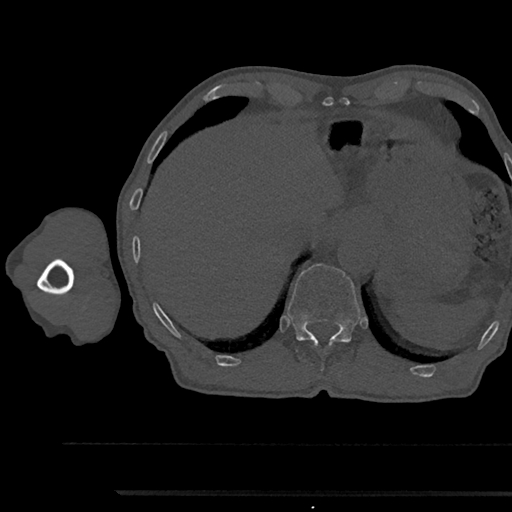
CT including the spine, one axial slice. Position 741 of 797 along the scan axis. Reconstruction kernel Br40s/3. Bone window (W 1800 / L 400 HU). 0.5 mm slice thickness. 512 × 512 image matrix, field of view 367 × 367 mm. Patient: male, 79 years. From the clinical record (not read from this slice): primary cancer: prostate.
Annotated regions visible in this slice (semi-automatically segmented with operator editing):
- T12 vertebra: bounding box (x1, y1, x2, y2) in pixels: (287, 264, 360, 359)